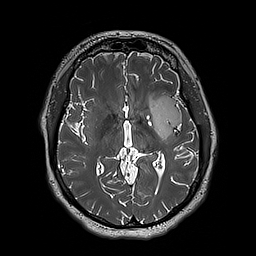
Brain MRI from a brain-tumour surgery series, one axial slice. Position 106 of 192 along the scan axis. 256 × 256 image matrix. From the clinical record (not read from this slice): histopathology: Astrocytoma; WHO grade: 3; IDH mutation: yes.
Outlined on this slice (outlined manually by an expert reader):
- tumour: bounding box (x1, y1, x2, y2) in pixels: (147, 95, 182, 141)